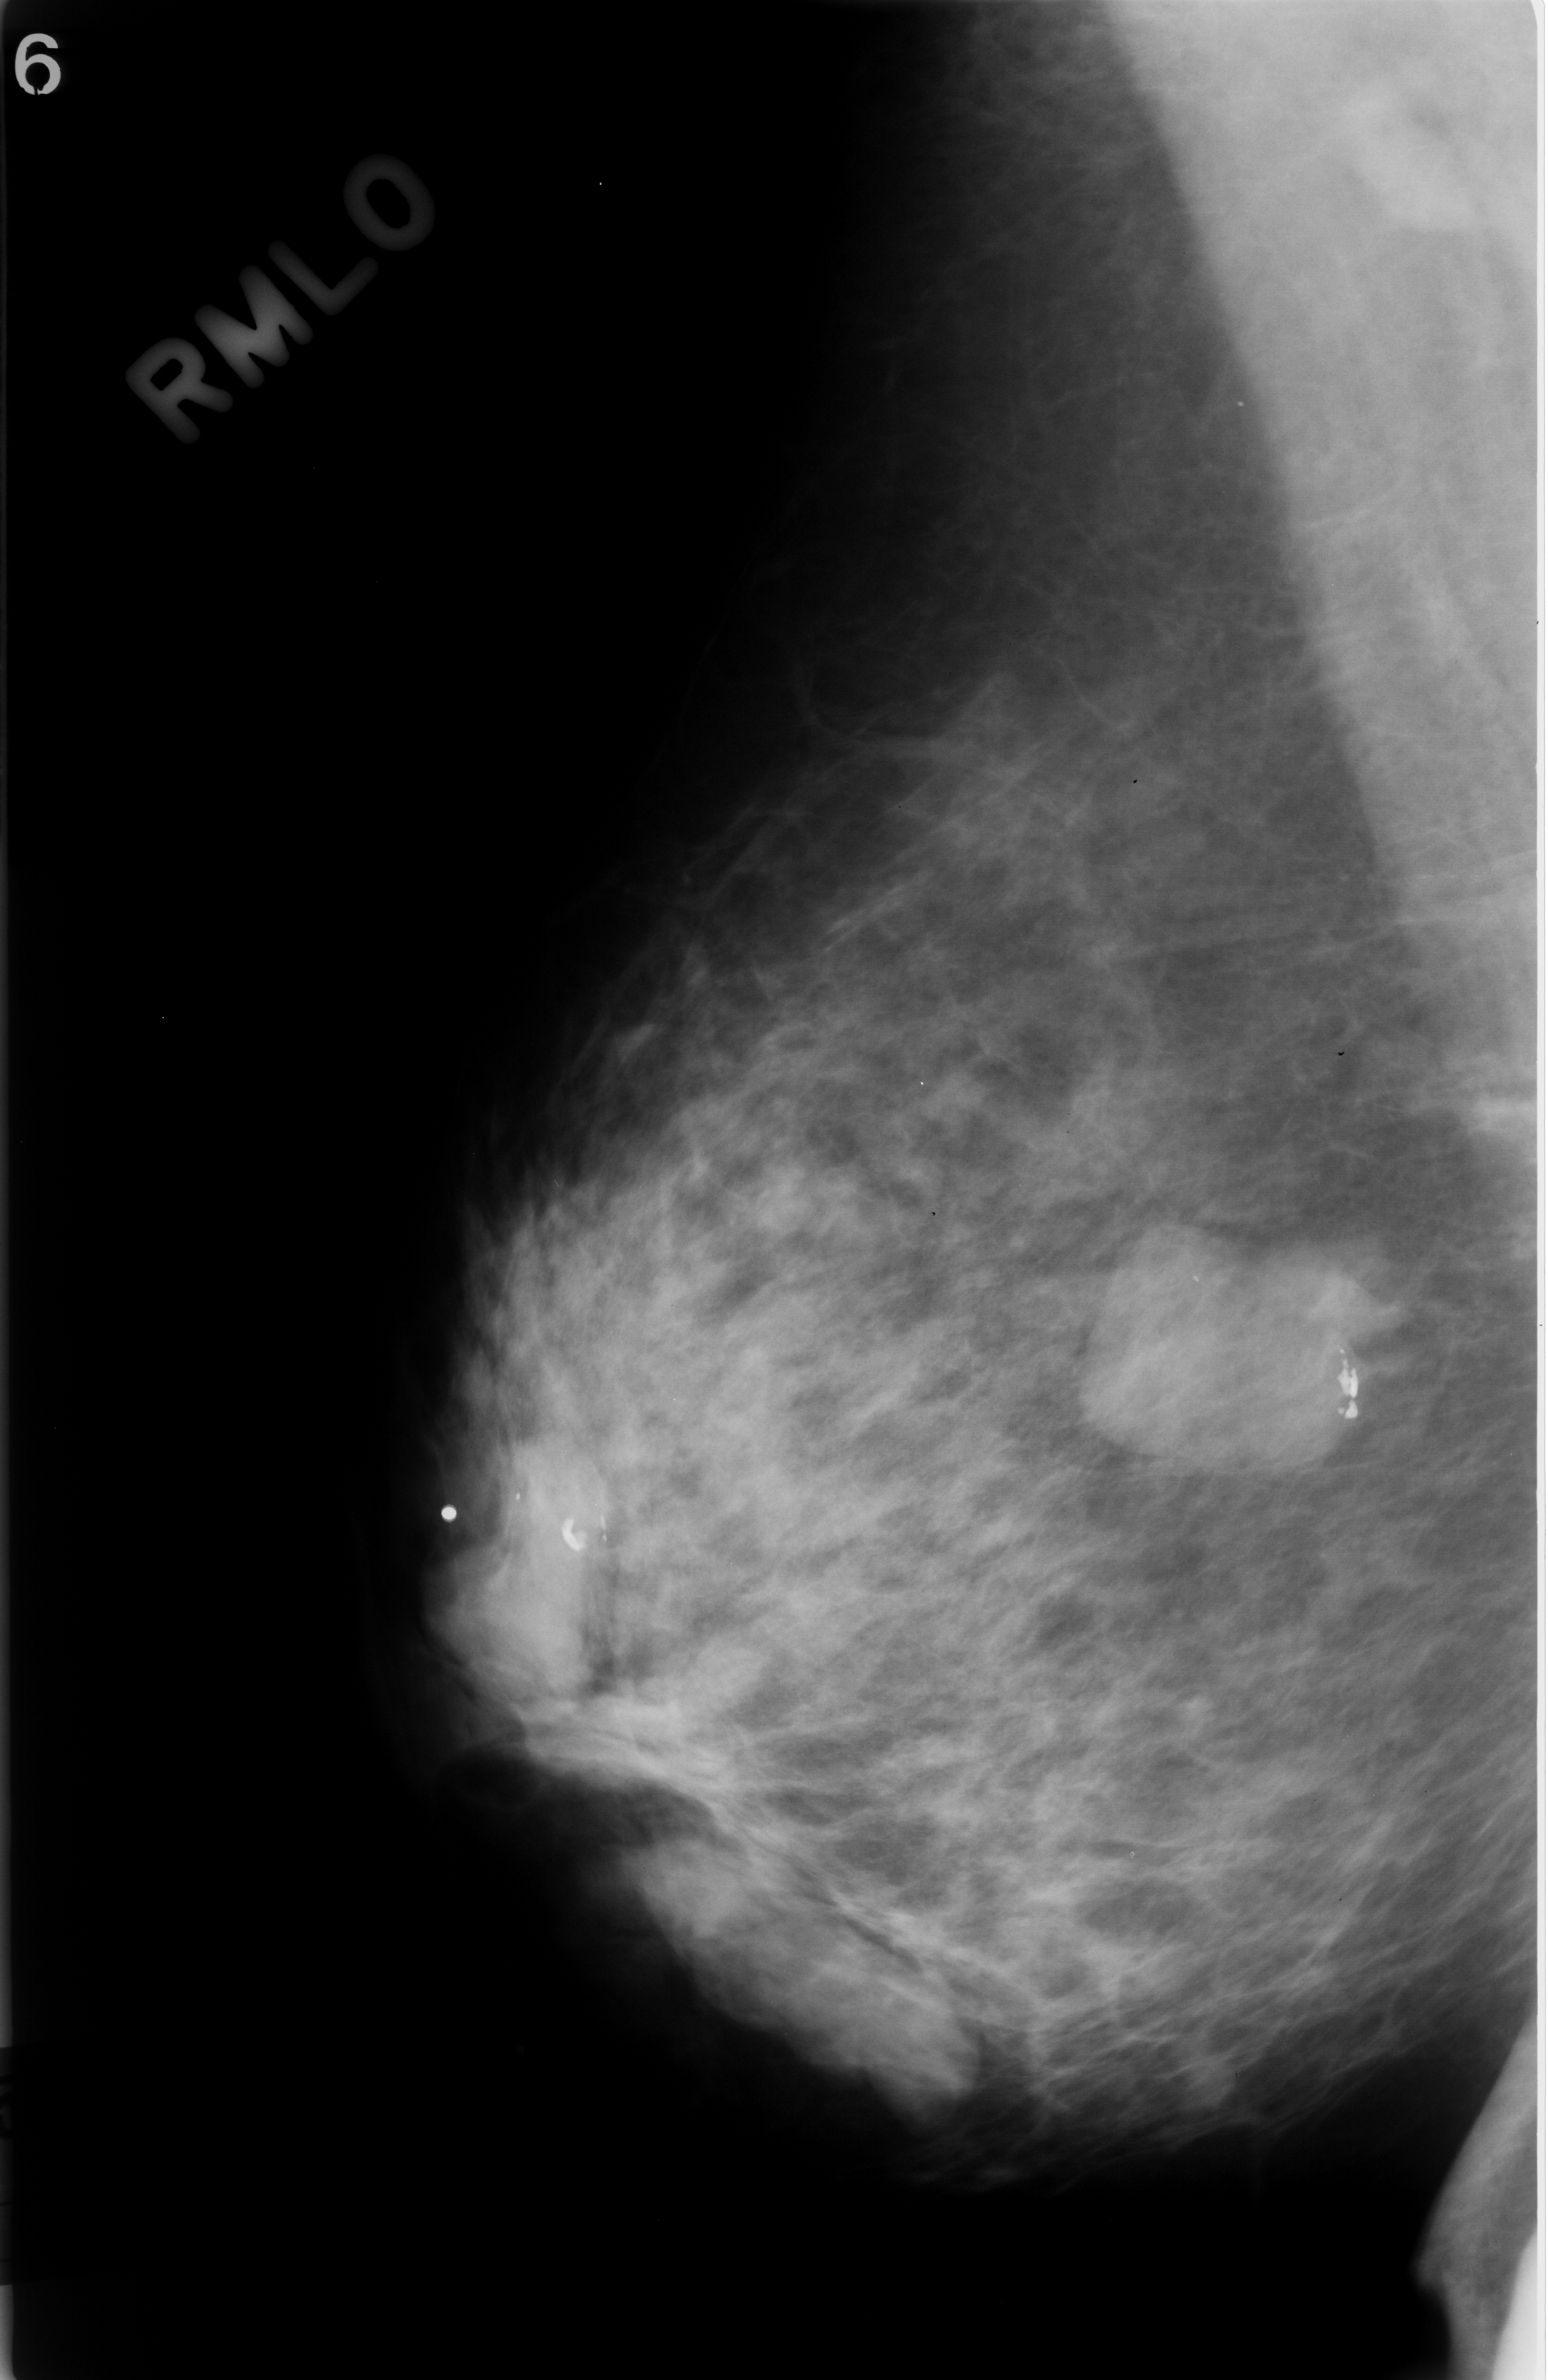
Digitized screen-film mammogram, right breast, mediolateral oblique (MLO) view, breast composition: scattered fibroglandular densities (BI-RADS density category 2 of 4).
Radiologist-marked abnormalities on this image: Finding 1 of 2: mass, shape lobulated, margins circumscribed; BI-RADS assessment category 3; subtlety rating 5 on a 1 (subtle) to 5 (obvious) scale; pathology result (as recorded, not read from the image): benign. Finding 2 of 2: mass, shape oval, margins circumscribed; BI-RADS assessment category 3; pathology result (as recorded, not read from the image): benign.